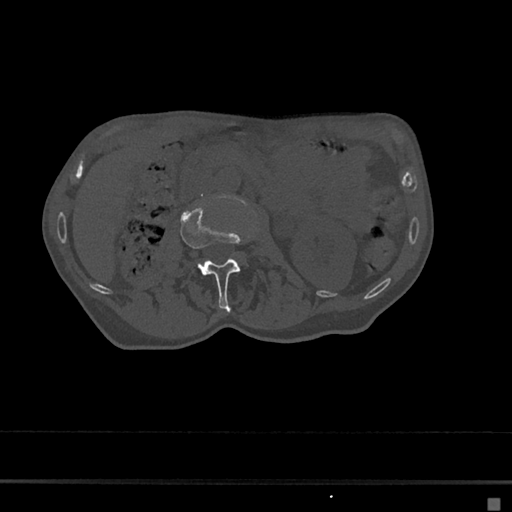
CT including the spine, one axial slice. Reconstruction kernel Br40s/3. 120 kVp. Bone window (W 1800 / L 400 HU). 0.5 mm slice thickness. 512 × 512 image matrix, field of view 360 × 360 mm. Patient: female, 68 years. From the clinical record (not read from this slice): primary cancer: renal.
Annotated regions visible in this slice (semi-automatic segmentation, software-assisted and operator-edited):
- L2 vertebra: bounding box <180,205,246,309> (left, top, right, bottom; pixels)